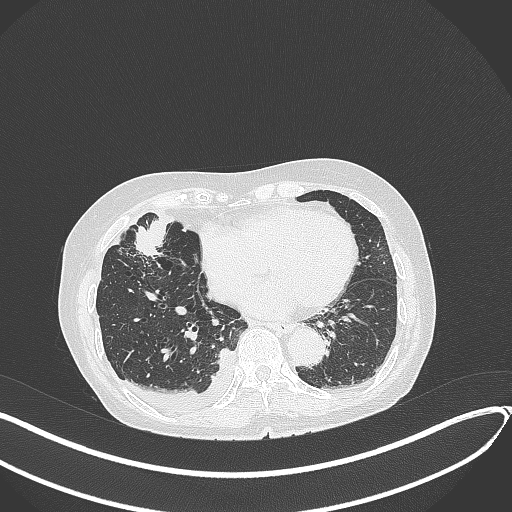
Chest CT, one axial slice. Slice 134 of 418 in the series (ordered by position). Reconstruction kernel B70f. 120 kVp. Lung window (W 1500 / L -600 HU). 1 mm slice thickness. 512 × 512 image matrix, field of view 400 × 400 mm. Patient: female, 75 years. Case-level facts recorded for this patient, not image findings: clinical TNM (as recorded): T2a N3 M0.
Outlined on this slice (rectangle marked by the reading radiologist):
- lung tumour (recorded histology: adenocarcinoma): bounding box [x1, y1, x2, y2] px = [132, 216, 172, 263]